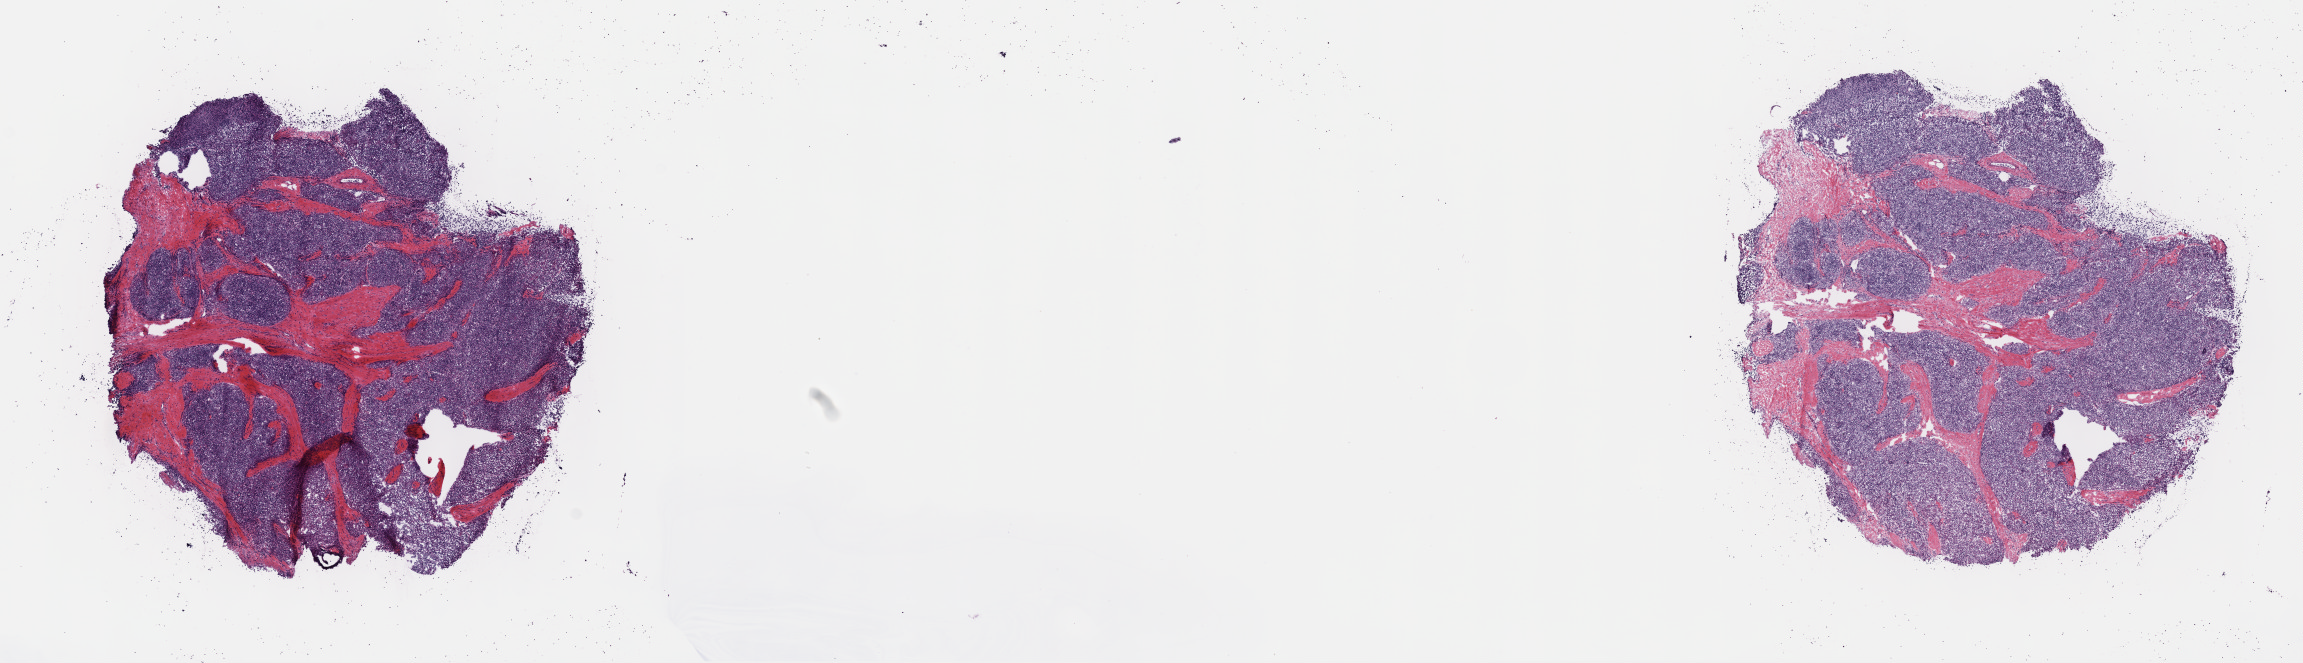
Whole-slide histology image, H&E — low-resolution overview of the scanned area, about 18.6 x 5.4 mm, frozen section from the top of the tissue portion, primary tumour sample from the thymus. Female patient; age at initial diagnosis 53 years. Slide review estimates, as recorded: tumour cells 70%, tumour nuclei 80%, normal cells 5%, stromal cells 25%, necrosis 0%. Infiltration values recorded for this section: lymphocyte infiltration 0%, monocyte infiltration 0%, neutrophil infiltration 0%.
Histologic diagnosis: Thymoma, type B2, malignant.